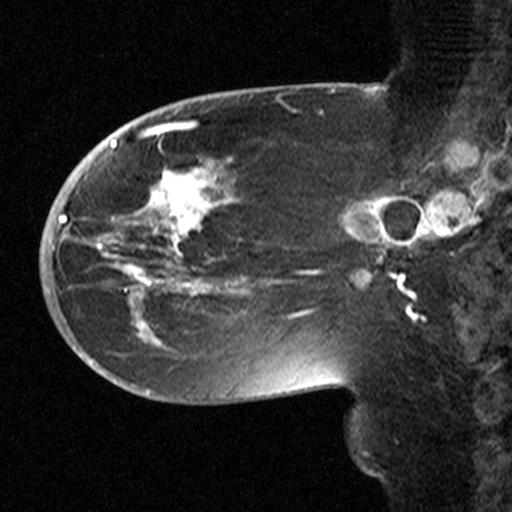
Breast MRI (dynamic contrast-enhanced), one sagittal slice; position 17 of 44 along the scan axis; dynamic contrast-enhanced study with each time point stored as its own series, time point 2 of 3 at this slice position (early post-contrast, ordered by acquisition time); 1.5 T; TE 4.5 ms, TR 11 ms; 512 × 512 image matrix, field of view 200 × 200 mm. Female patient, age 53 years. Case-level facts recorded for this patient, not image findings: setting: breast cancer imaged before/during neoadjuvant chemotherapy; receptor status: HR-positive, HER2-negative.
Annotated regions visible in this slice (semi-automatically segmented with operator editing):
- analysis volume of interest (the breast-tissue region the enhancement analysis was run in; not a lesion): bounding box <58,154,311,367> (left, top, right, bottom; pixels)
- tumour enhancement mask (voxels above the 90 % enhancement threshold inside the analysis volume of interest): <60,166,310,335>